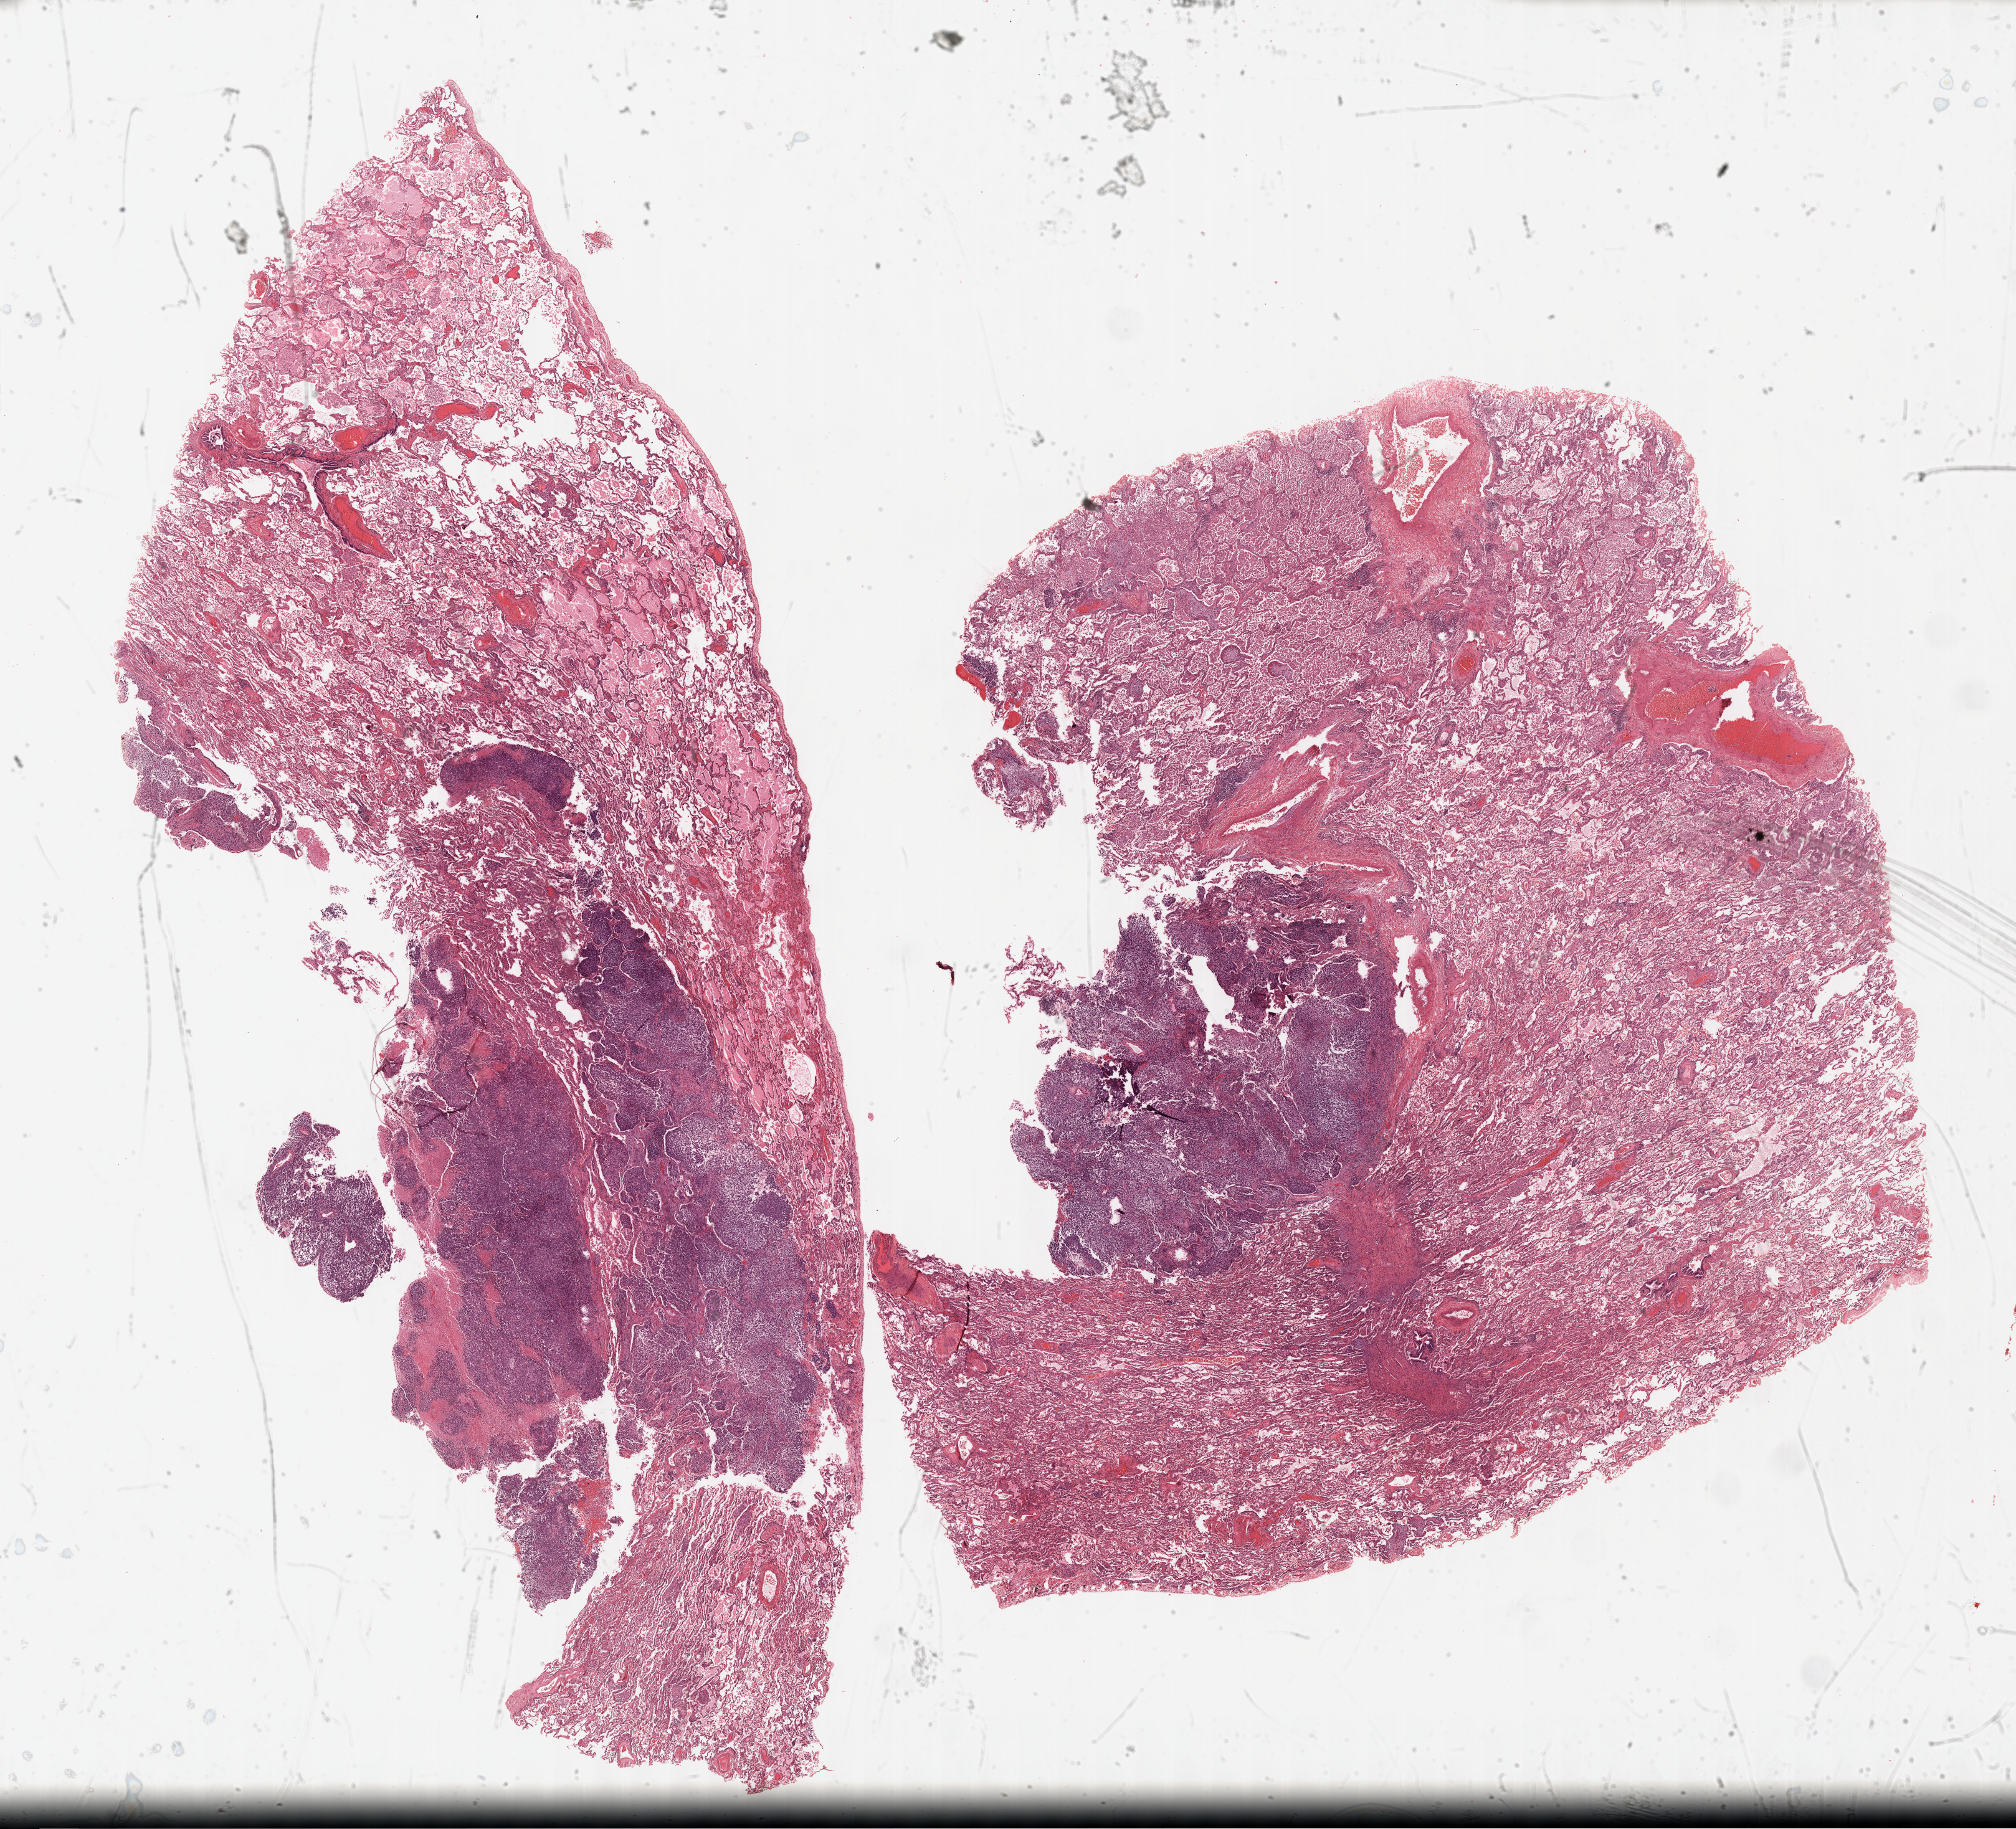
Whole-slide histology image, H&E, low-resolution overview of the scanned area, about 26.2 x 23.7 mm (from a 40x scan); formalin-fixed paraffin-embedded (FFPE) diagnostic section; metastatic tumour sample, sampled site: lower lobe, lung. Female patient; age at initial diagnosis 60 years.
This section: metastatic tumour tissue. Patient diagnosis: Malignant melanoma, NOS.